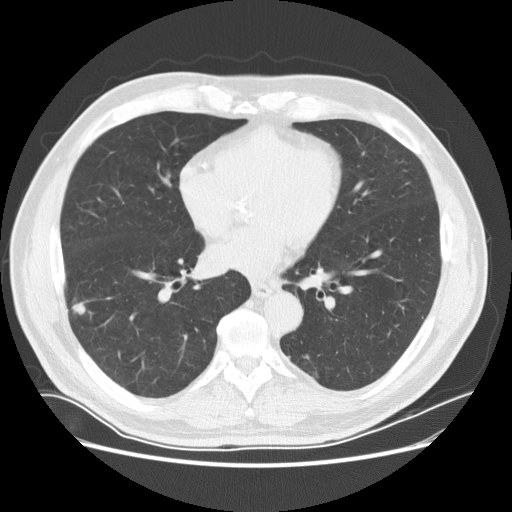
Chest CT (low-dose screening protocol), one axial image. First (baseline) screen. Lung window (W 1500 / L -600 HU). 2.5 mm slice thickness. Standard (soft-tissue) reconstruction kernel (STANDARD). 120 kVp. Slice 93 of 170 in the series. 512 × 512 image matrix. Male participant, aged 72 years at enrolment. Current smoker at enrolment.
- Expert-annotated lung lesion, bounding box (x1, y1, x2, y2) in pixels: (61, 293, 94, 325).
- The exam's reader record, not a measurement of the box and not confirmed to be the same lesion: non-calcified nodule or mass ≥4 mm, right lower lobe, 13 × 8 mm, poorly defined margins, soft tissue attenuation.
- Official screen result: positive, change unspecified: nodule(s) >= 4 mm or enlarging nodule(s), mass(es), or other non-specific abnormalities suspicious for lung cancer.
- Lung cancer was diagnosed 17 days after this screen: non-small cell carcinoma, right lower lobe, moderately differentiated (G2), stage IA (AJCC 6th edition), 10 mm at pathology.